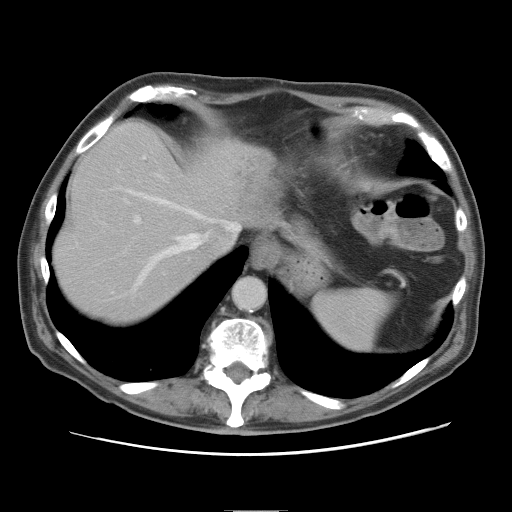
Contrast-enhanced abdominal CT, one axial slice; slice 66 of 89 in the series (ordered by position); soft-tissue window (W 400 / L 40 HU); 5 mm slice thickness; 512 × 512 image matrix, field of view 375 × 375 mm. Male patient, age 69 years. From the clinical record (not read from this slice): diagnosis: colorectal cancer liver metastases, imaged before liver resection; multiple liver metastases: no; largest metastasis: 8.5 cm; chemotherapy before resection: no.
Annotated regions visible in this slice (manually delineated by an expert):
- hepatic veins: bounding box <116,173,240,283> (left, top, right, bottom; pixels)
- liver: <55,124,258,322>
- planned liver remnant (the part of the liver to remain after resection): <55,124,239,322>
- portal vein (with intrahepatic branches): <134,156,145,224>